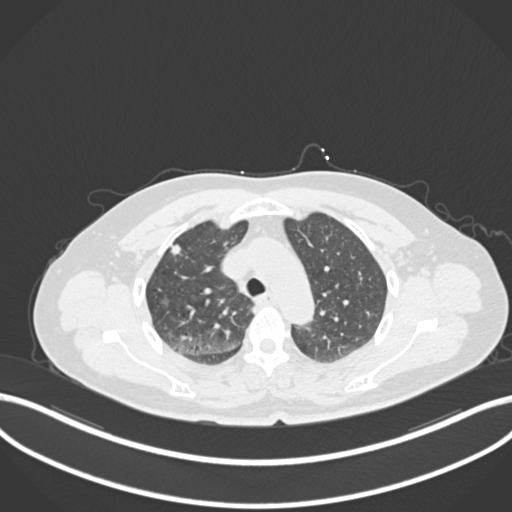
Chest CT, one axial slice. Position 172 of 223 along the scan axis. 120 kVp. Lung window (W 1500 / L -600 HU). 1 mm slice thickness. 512 × 512 image matrix, field of view 400 × 400 mm. Female patient, age 56 years. Case-level facts recorded for this patient, not image findings: clinical TNM (as recorded): T1c N0 M0.
Annotated regions visible in this slice (bounding box drawn by a radiologist):
- lung tumour (recorded histology: adenocarcinoma): bounding box <167,241,185,256> (left, top, right, bottom; pixels)